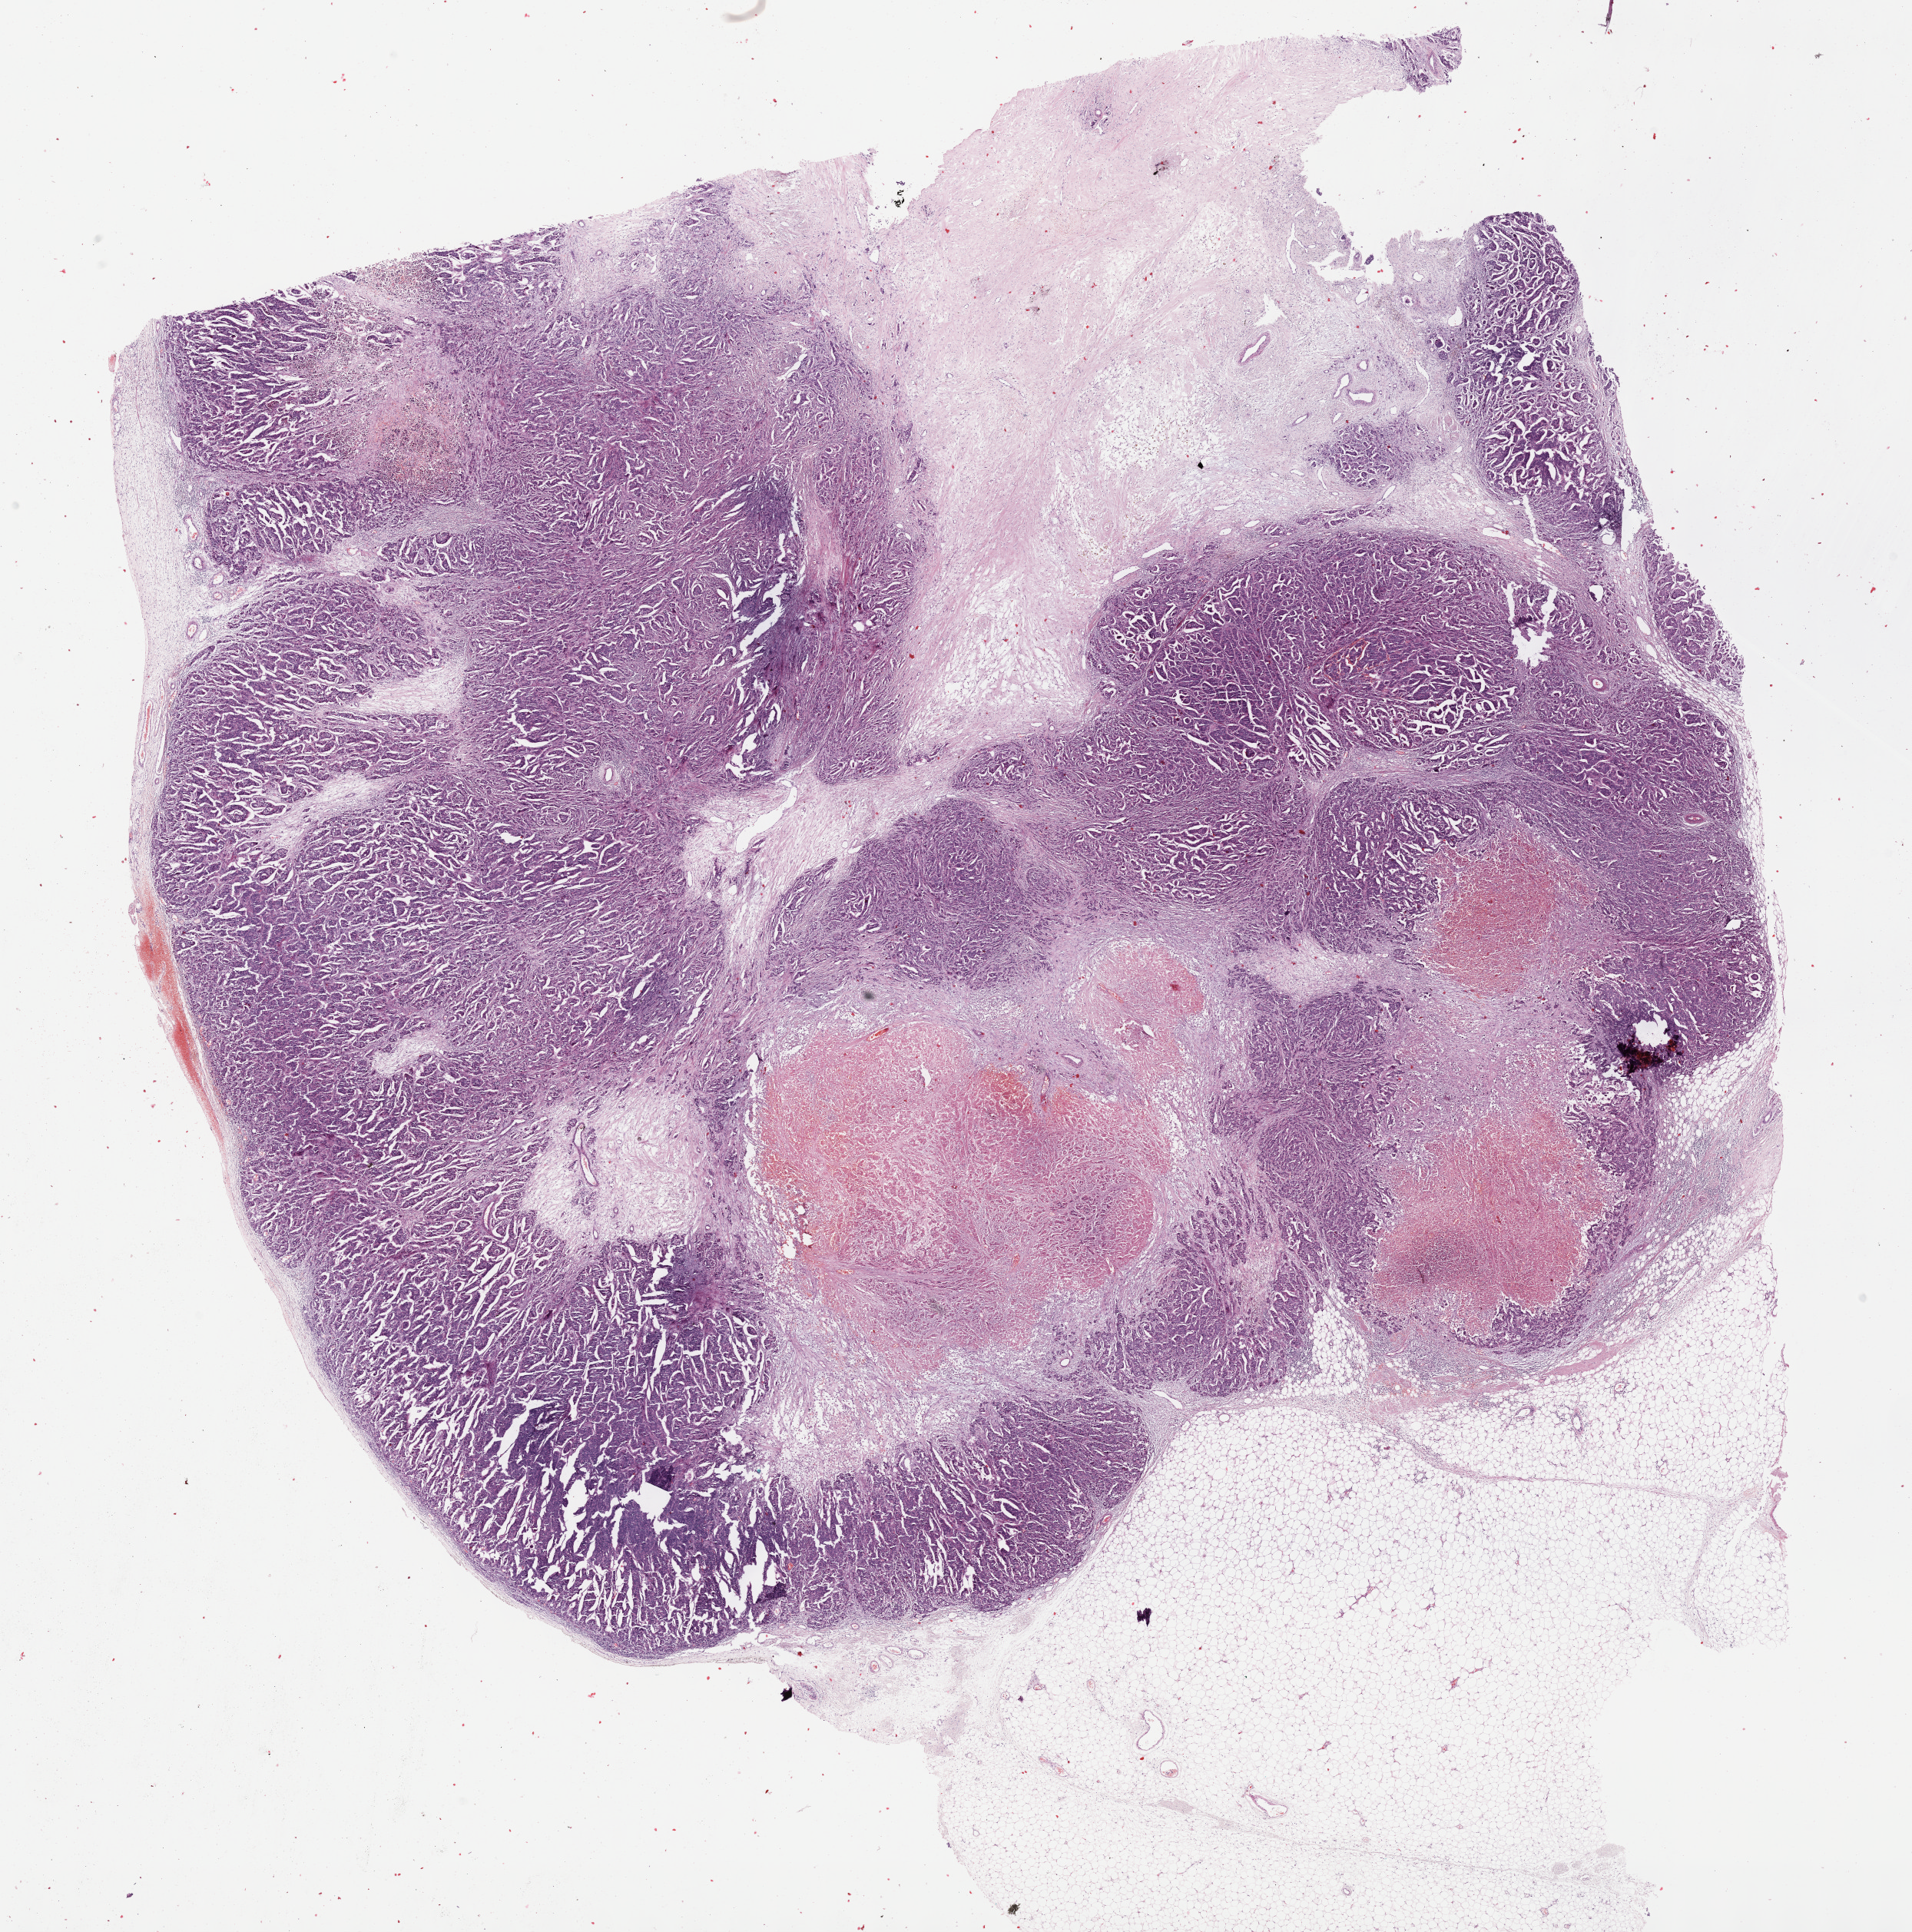
Whole-slide histology image, H&E-stained — a low-resolution overview of the entire scanned area, about 20.1 x 20.3 mm (slide scanned at 40x), FFPE section, sample: primary tumour, breast. Female, age 80 years at initial diagnosis.
AJCC pathologic stage: IIIA (7th edition). Histologic diagnosis: Infiltrating duct carcinoma, NOS. Laterality: left. Lymph nodes positive (case pathology): 5 of 7 examined.